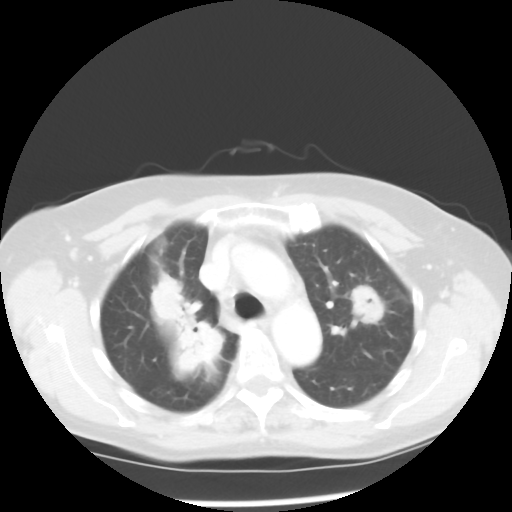
Chest CT, one axial slice. Slice 37 of 52 in the series (ordered by position). Reconstruction kernel STANDARD. Lung window (W 1500 / L -600 HU). 512 × 512 image matrix, field of view 328 × 328 mm. Female patient, age 60 years. Case-level facts recorded for this patient, not image findings: clinical TNM (as recorded): T2 N1 M1a.
Structures marked on this image (bounding box drawn by a radiologist):
- lung tumour (recorded histology: adenocarcinoma): box from (x=146, y=268) to (x=230, y=380) px